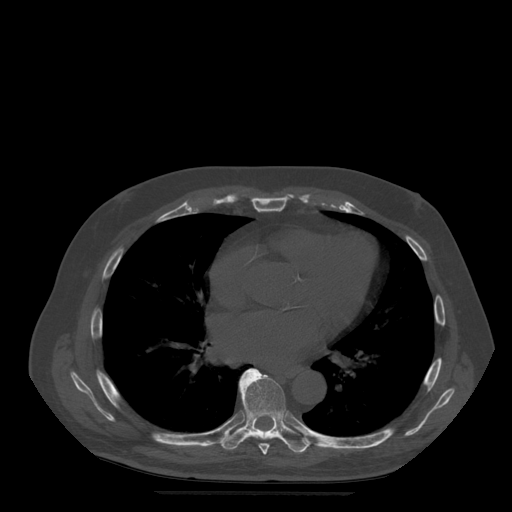
CT including the spine, one axial slice. Position 319 of 522 along the scan axis. Bone window (W 1800 / L 400 HU). 1.25 mm slice thickness. 512 × 512 image matrix, field of view 420 × 420 mm. Patient age 72 years. Case-level facts recorded for this patient, not image findings: primary cancer: prostate.
Outlined on this slice (semi-automatically segmented with operator editing):
- T7 vertebra: bounding box (x1, y1, x2, y2) in pixels: (243, 394, 270, 455)
- T8 vertebra: (220, 369, 310, 454)